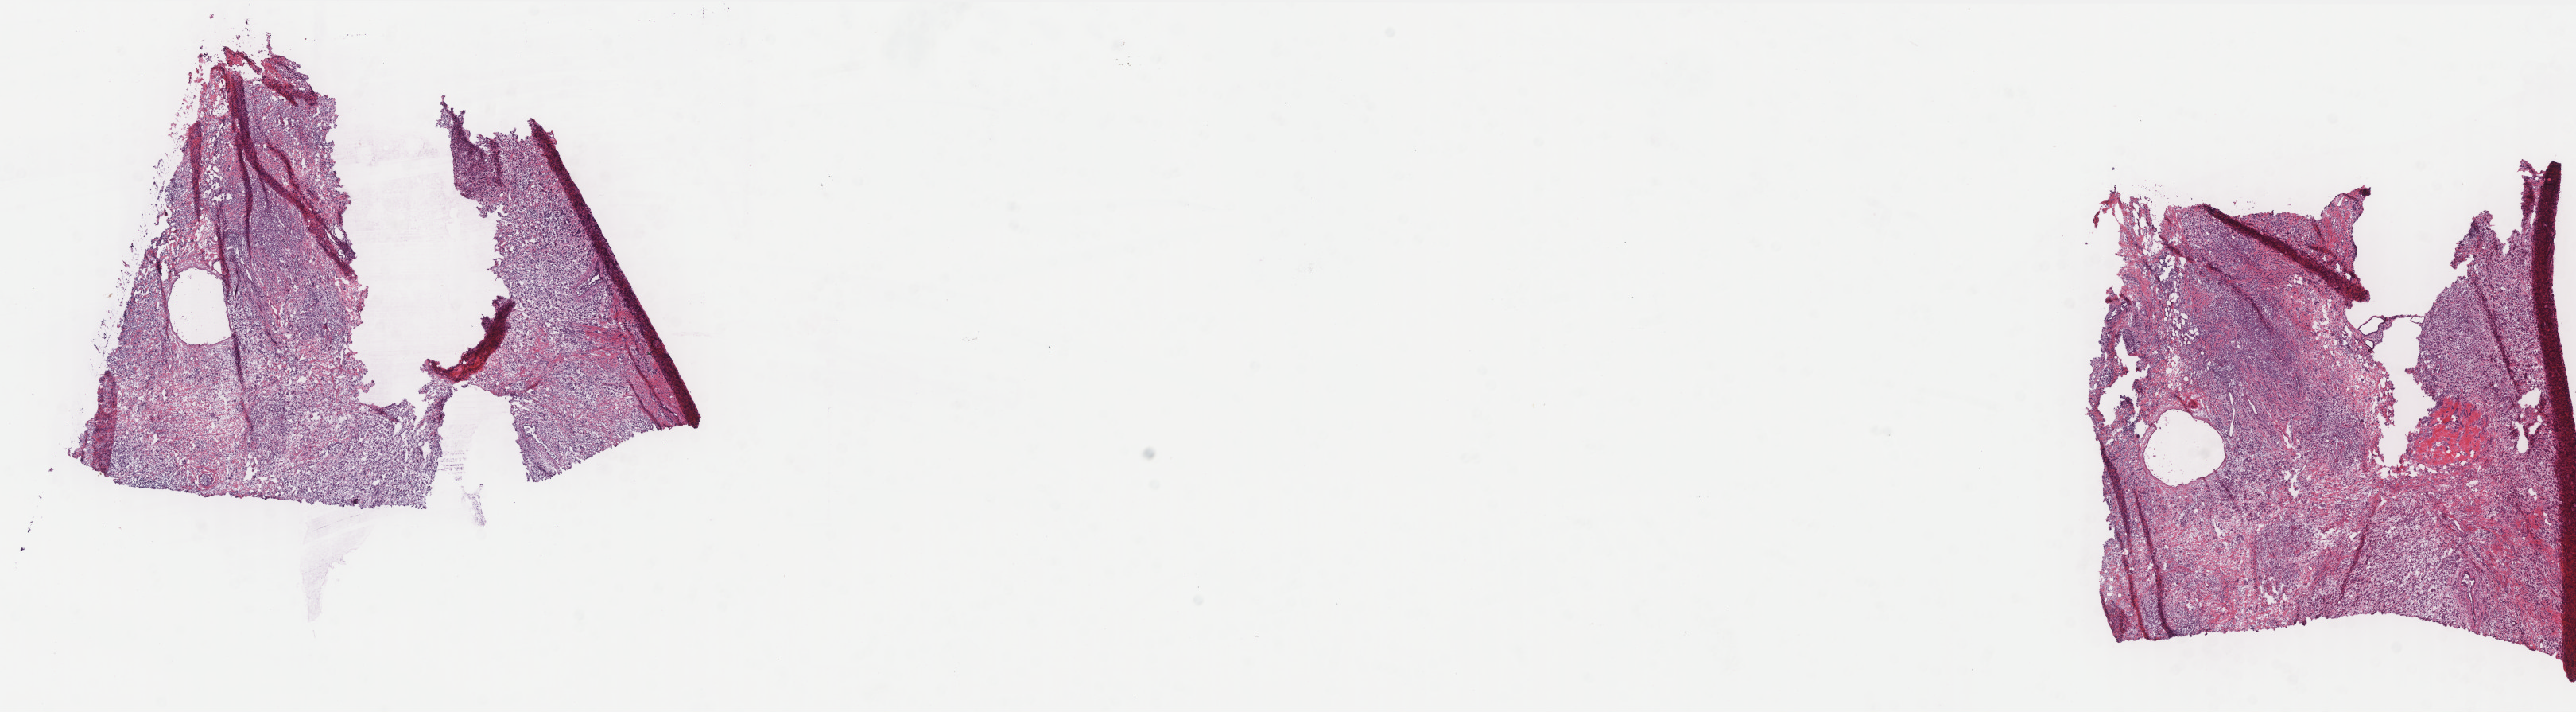
Whole-slide histology image, Hematoxylin and eosin (H&E) stained — whole scanned area (about 26.0 x 7.2 mm) shown as a low-resolution overview. Frozen section from the top of the tissue portion. Breast, primary tumour sample. Patient: female, age at initial diagnosis 34 years. Pathologist review of this section (percent, as recorded): tumour cells 85%, tumour nuclei 60%, normal cells 6%, stromal cells 8%, necrosis 1%. Inflammatory infiltration, as recorded: lymphocyte infiltration 20%, monocyte infiltration 0%, neutrophil infiltration 0%.
AJCC pathologic stage: IIIA (6th edition). Pathologic diagnosis: Infiltrating duct carcinoma, NOS.